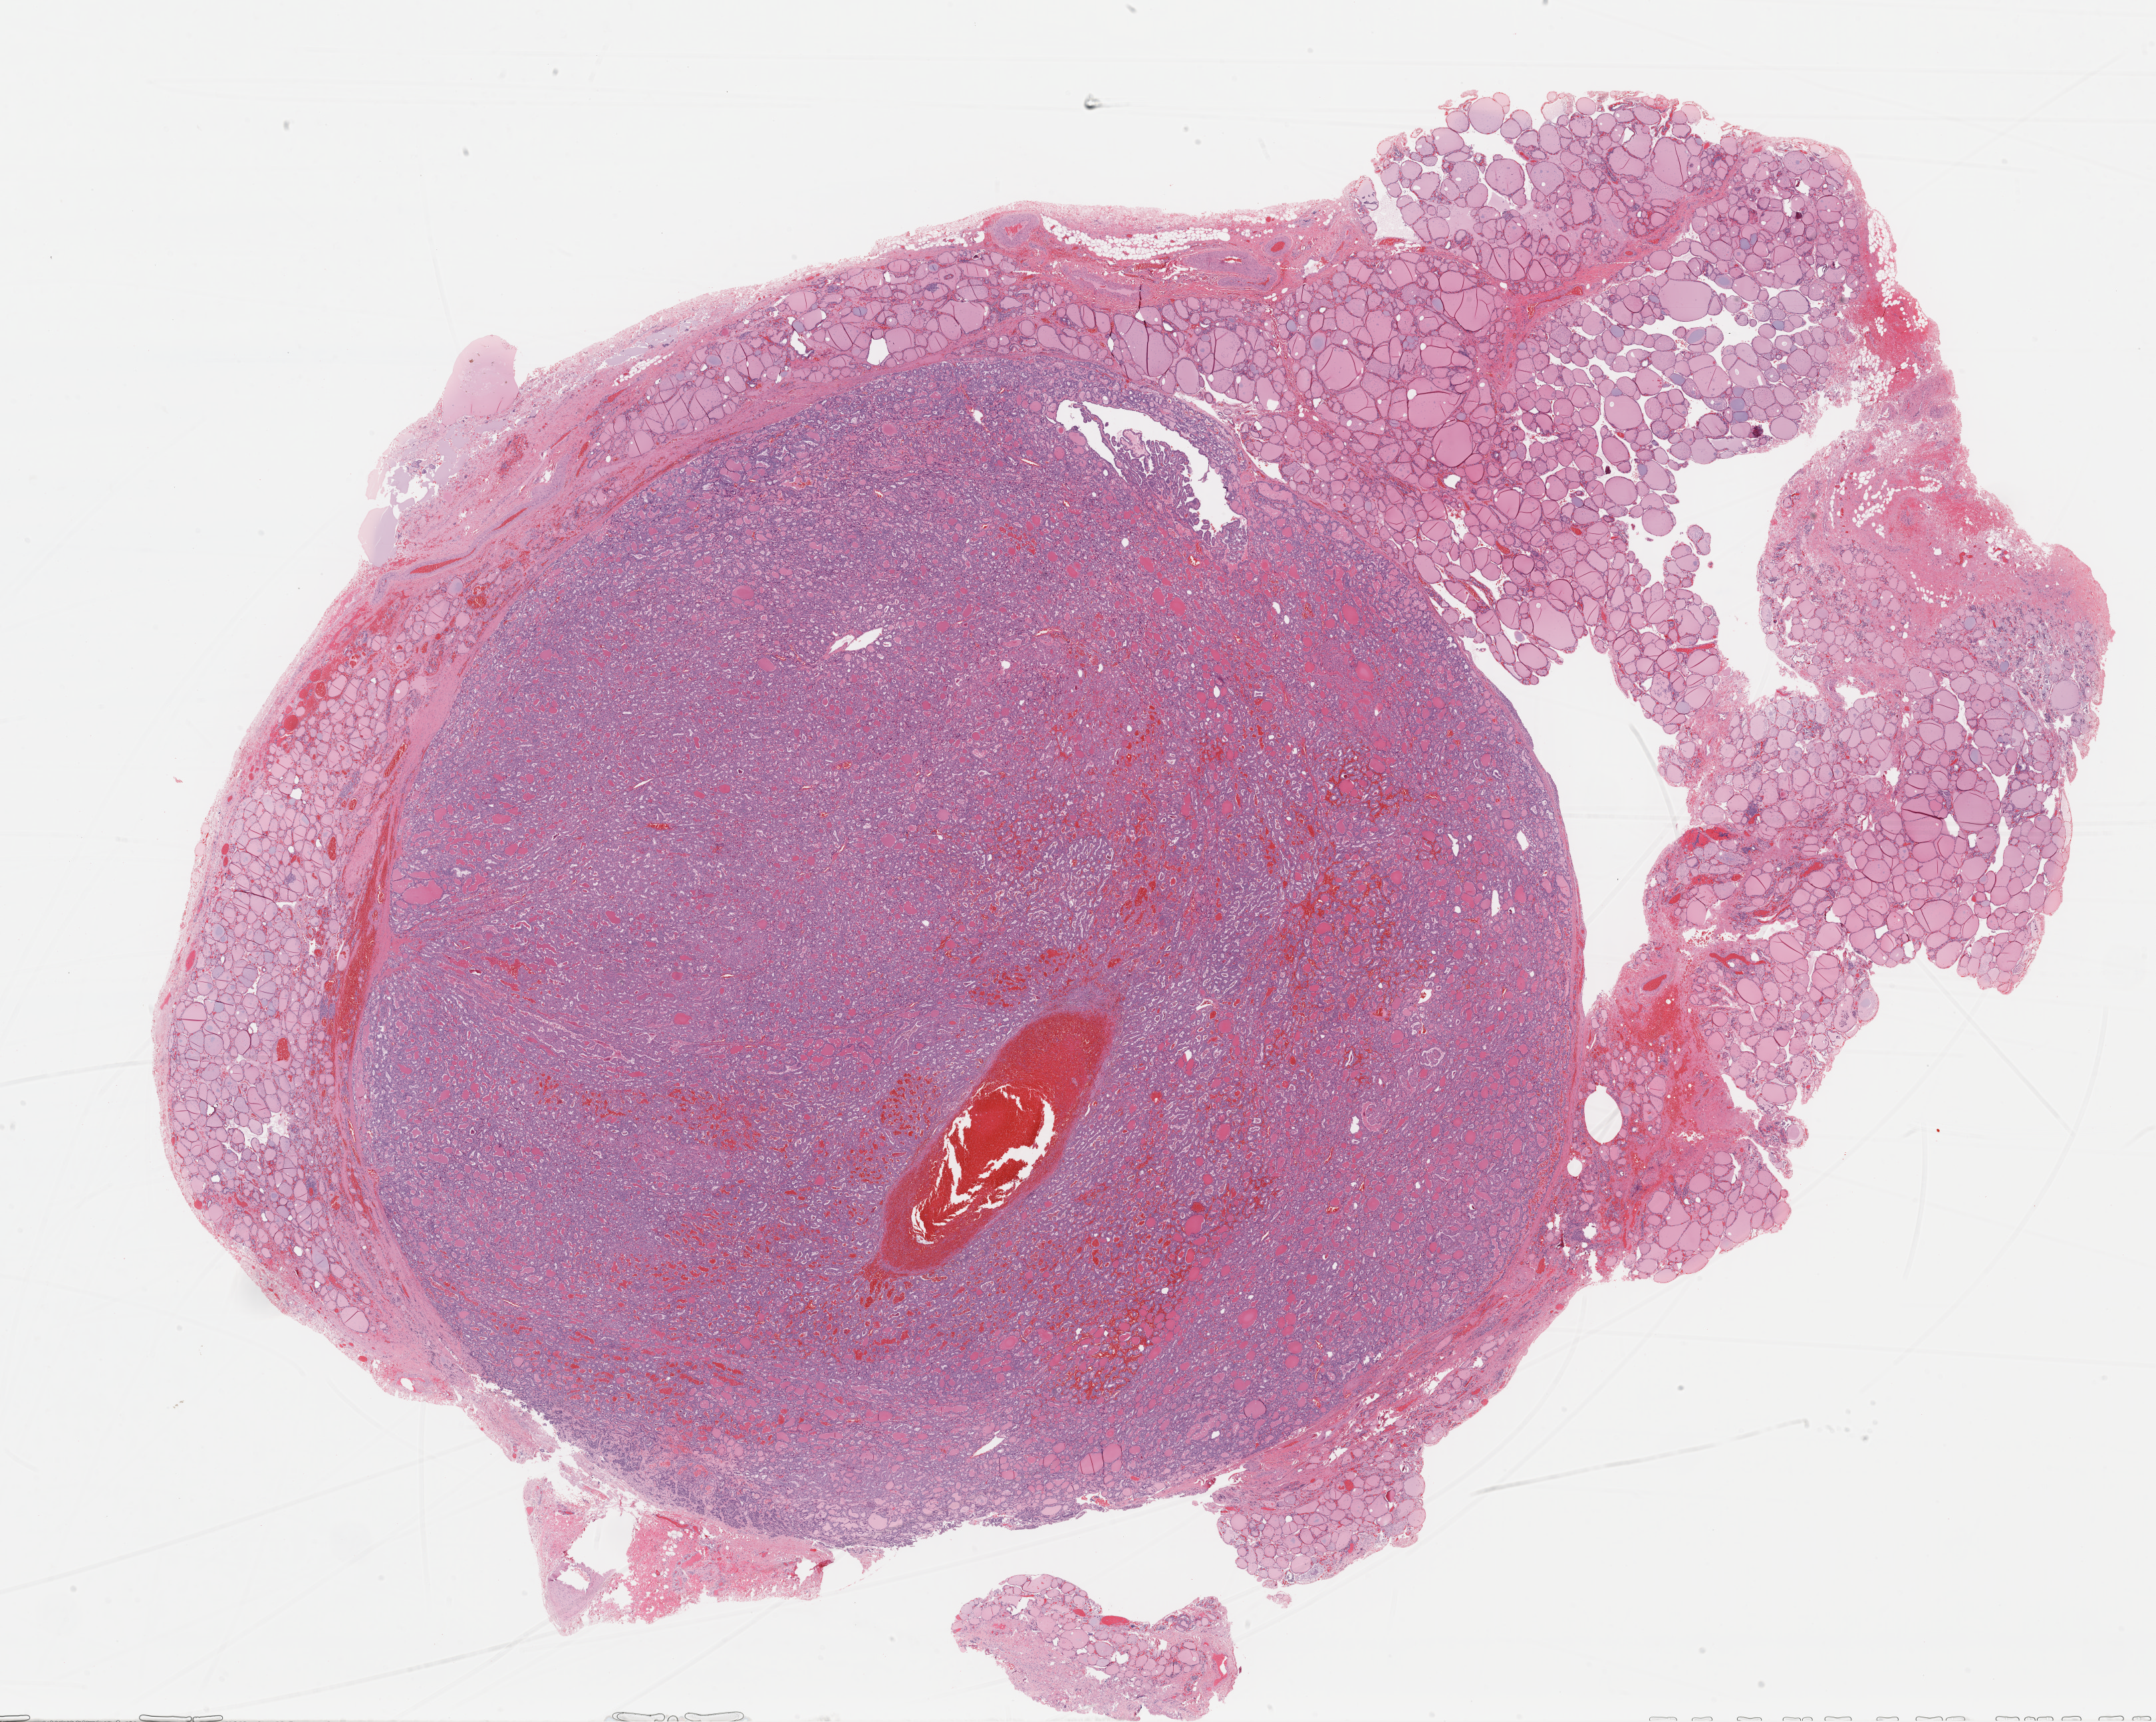
H&E-stained whole-slide image — a low-resolution overview of the entire scanned area, about 25.5 x 20.4 mm (from a 40x scan), FFPE section, thyroid, primary tumour sample. Female patient; age at initial diagnosis 55 years.
Pathologic diagnosis: Papillary adenocarcinoma, NOS (thyroid gland). AJCC pathologic stage: II (6th edition). Lymph nodes positive (case pathology): 0 of 1 examined.